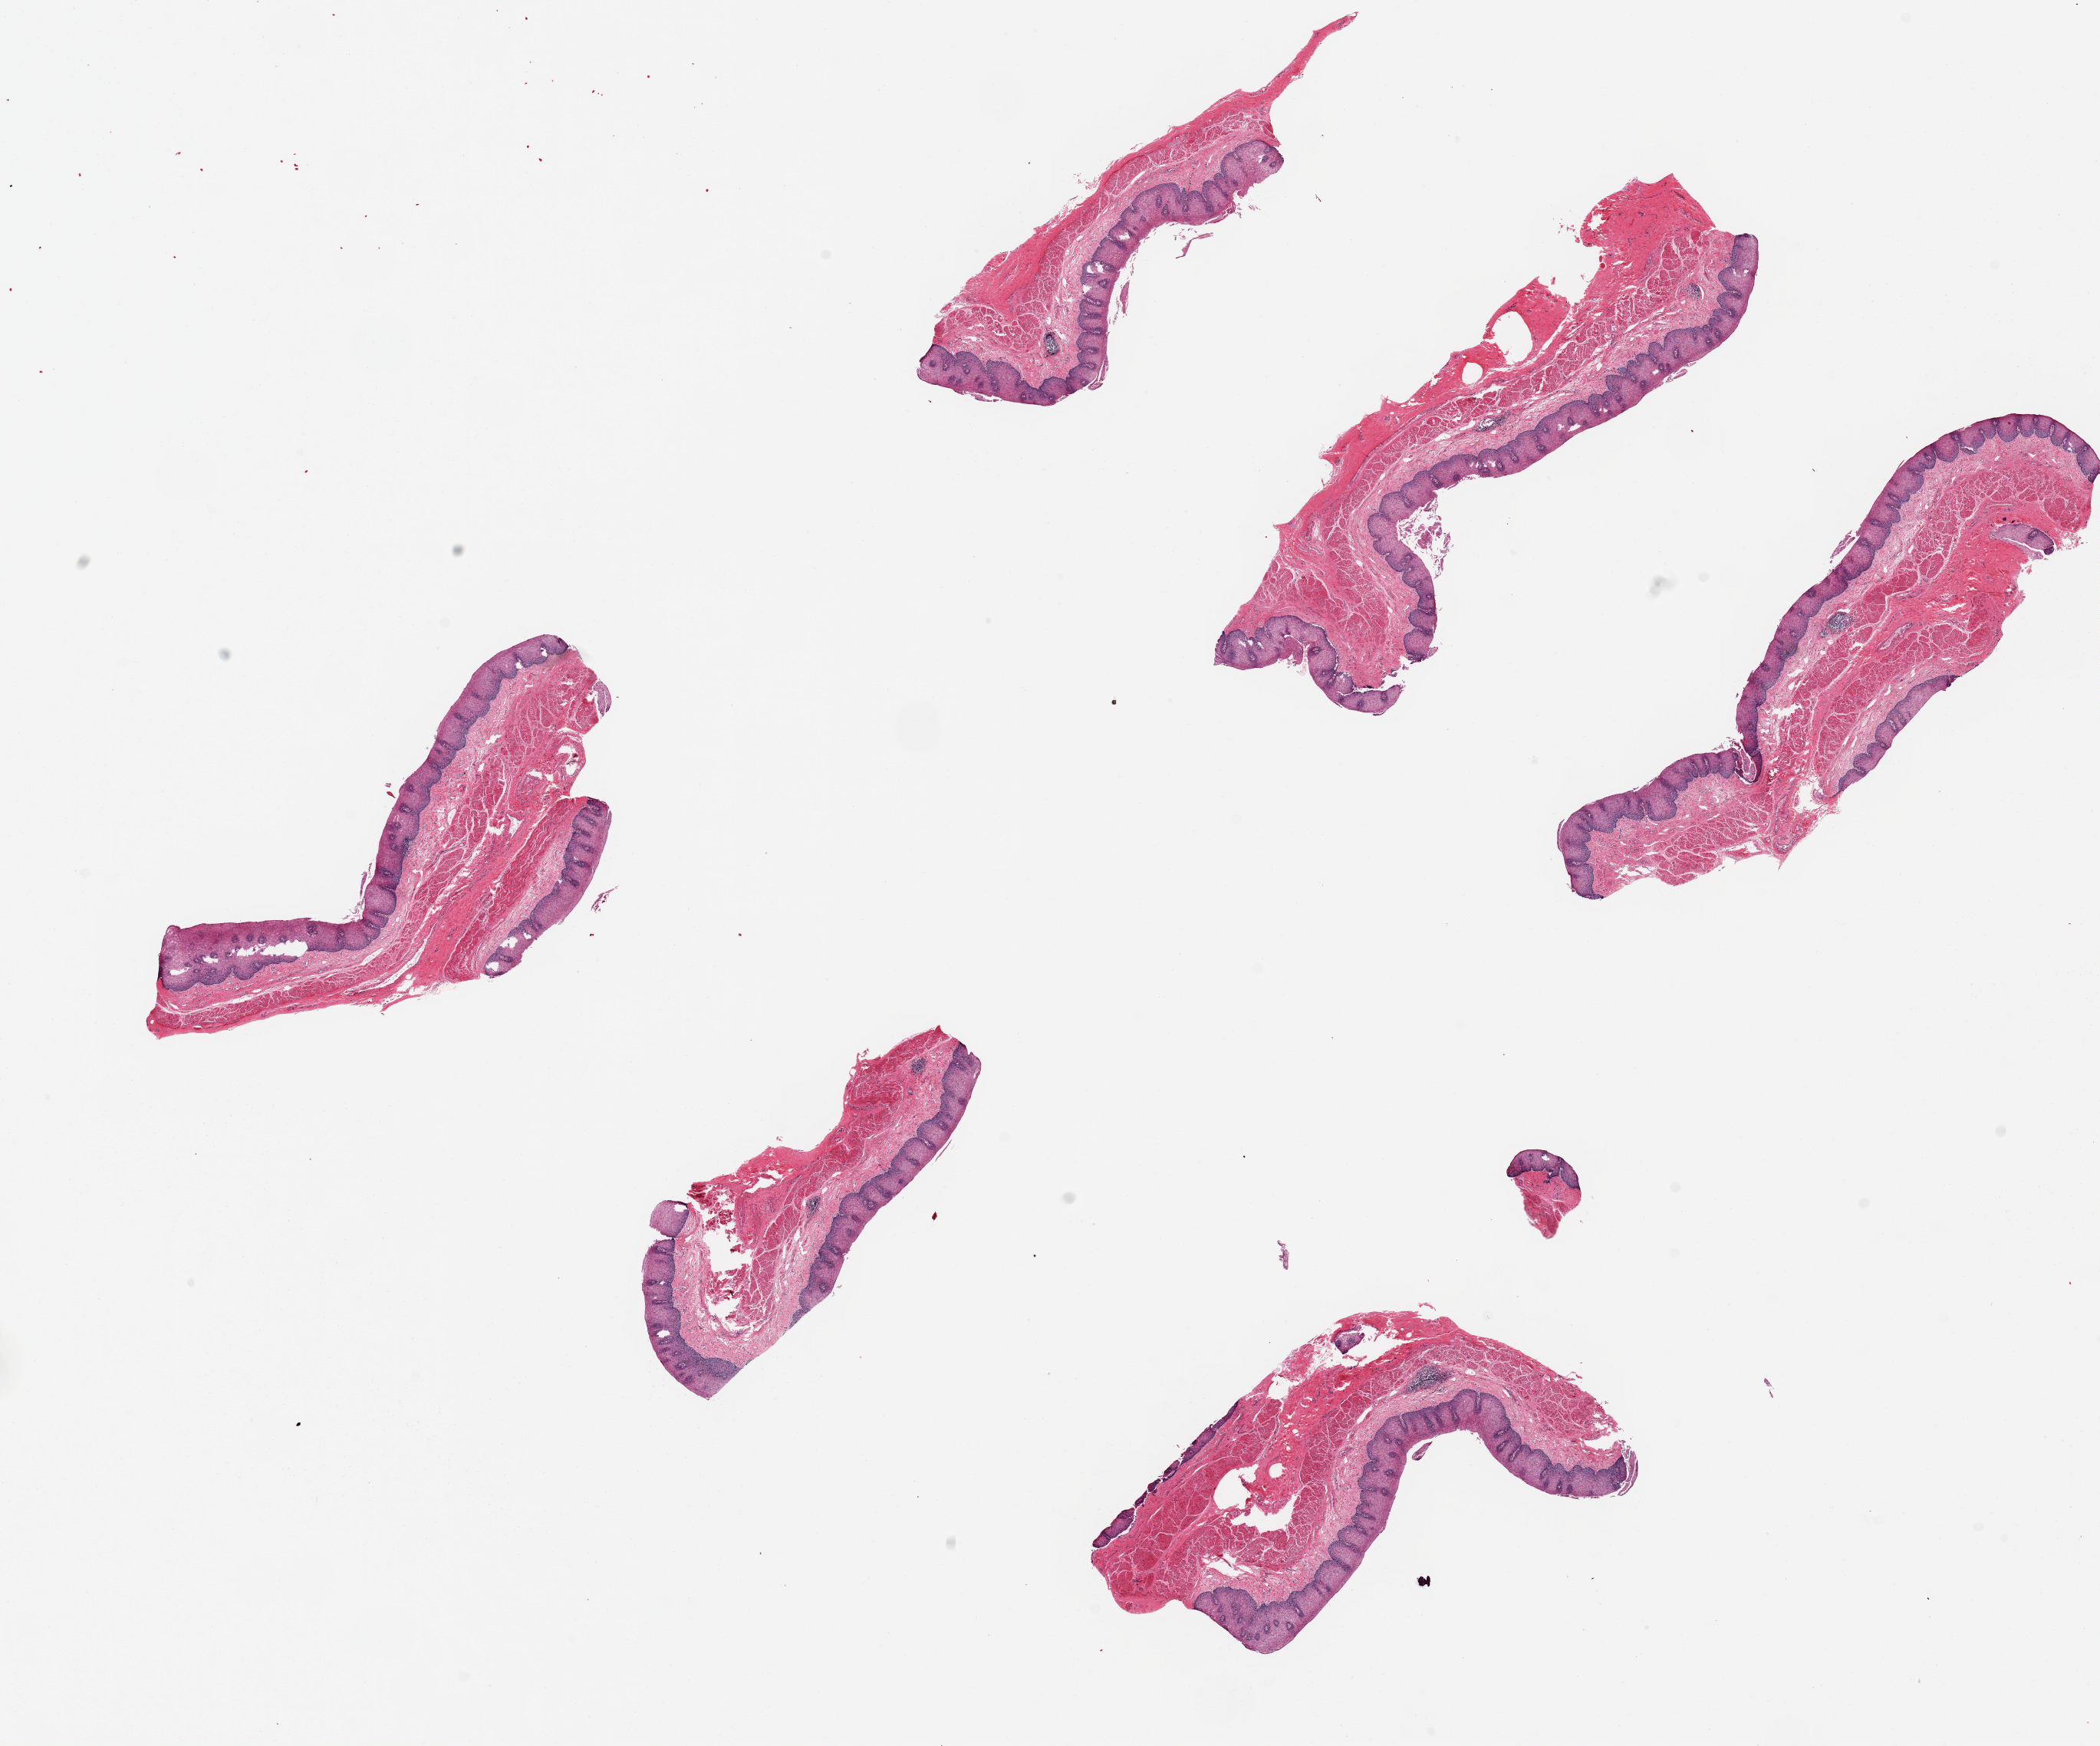
Whole-slide image, H&E stain — low-resolution overview of the scanned area, about 21.7 x 18.0 mm (from a 20x scan), PAXgene-fixed paraffin-embedded (PFPE) section, target tissue: esophageal mucous membrane, donor tissue sample. Donor sex: male.
- reviewer comment on this tissue sample: 6 pieces up to 7x1.8 mm